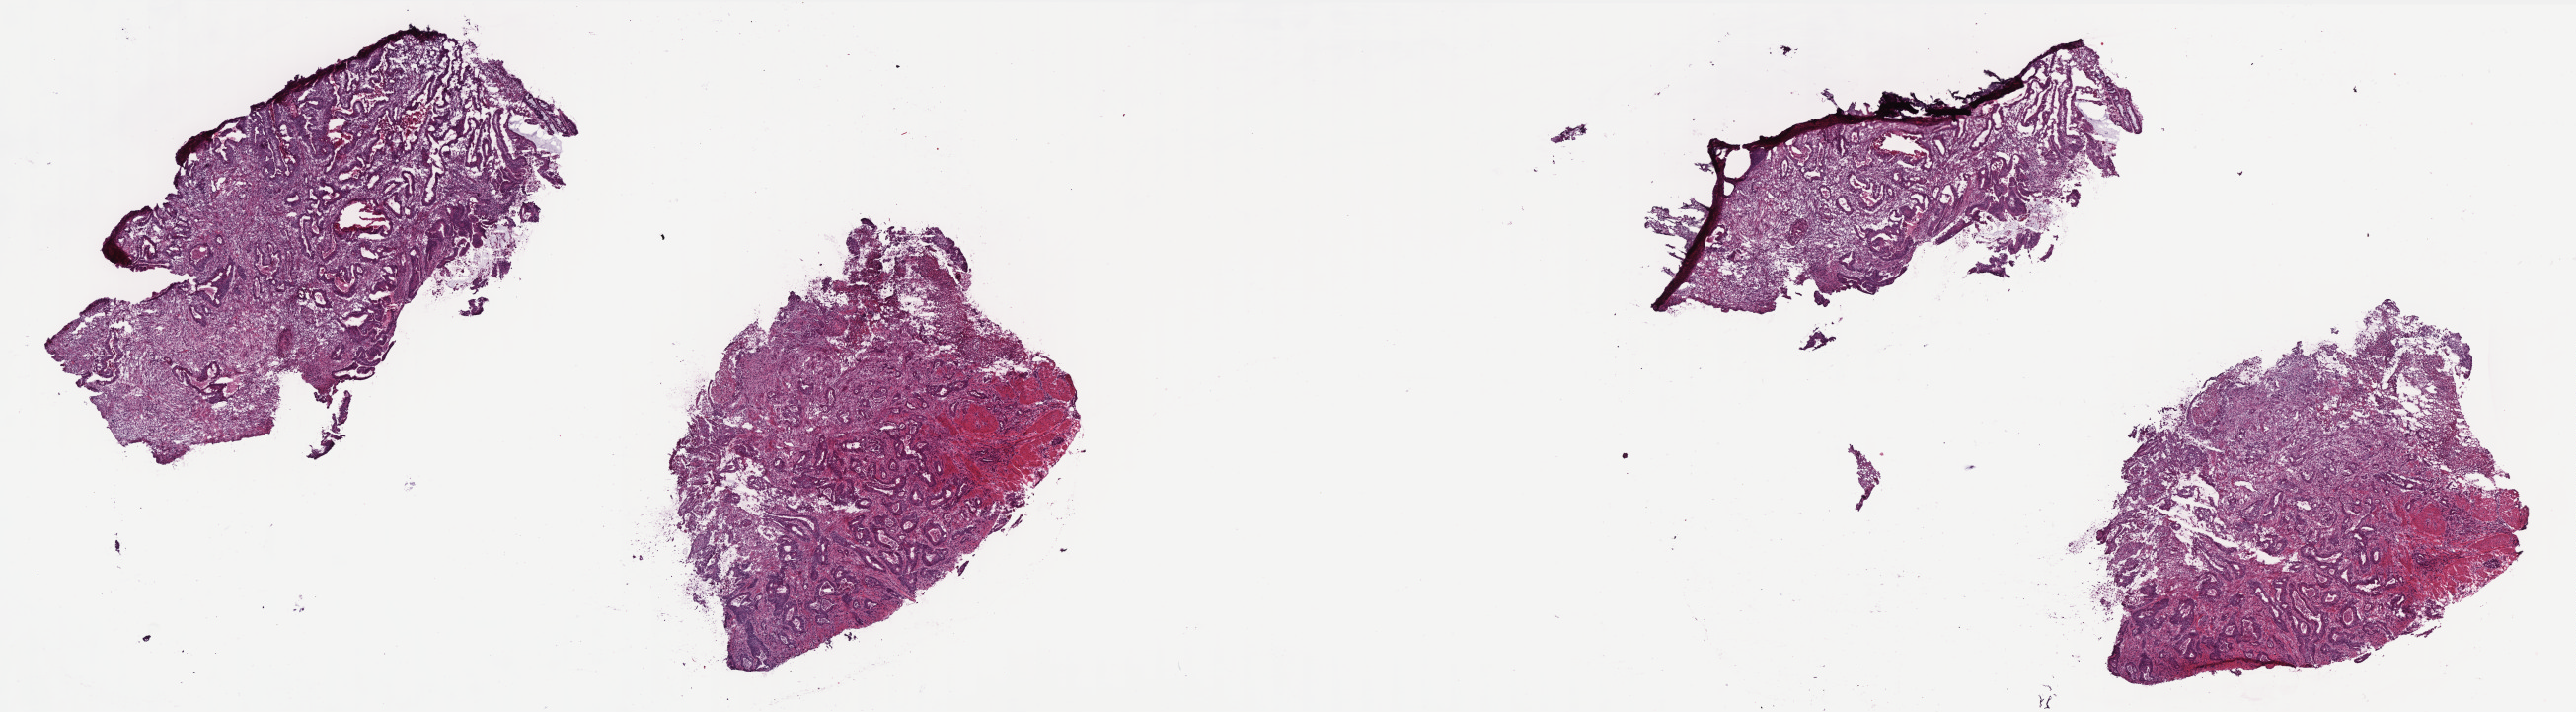
Whole-slide histology image, Hematoxylin and eosin (H&E) stained — whole scanned area (about 20.9 x 5.8 mm) shown as a low-resolution overview. Frozen section from the top of the tissue portion. Colon, primary tumour sample. Female patient; age at initial diagnosis 74 years. Composition of this section per pathologist review: tumour cells 80%, tumour nuclei 70%, normal cells 5%, stromal cells 10%, necrosis 5%. Inflammatory infiltration, as recorded: lymphocyte infiltration 6%, monocyte infiltration 1%, neutrophil infiltration 20%.
* AJCC pathologic stage: IIIC (6th edition)
* histologic diagnosis: Adenocarcinoma, NOS
* lymph nodes positive (case pathology): 4 of 35 examined